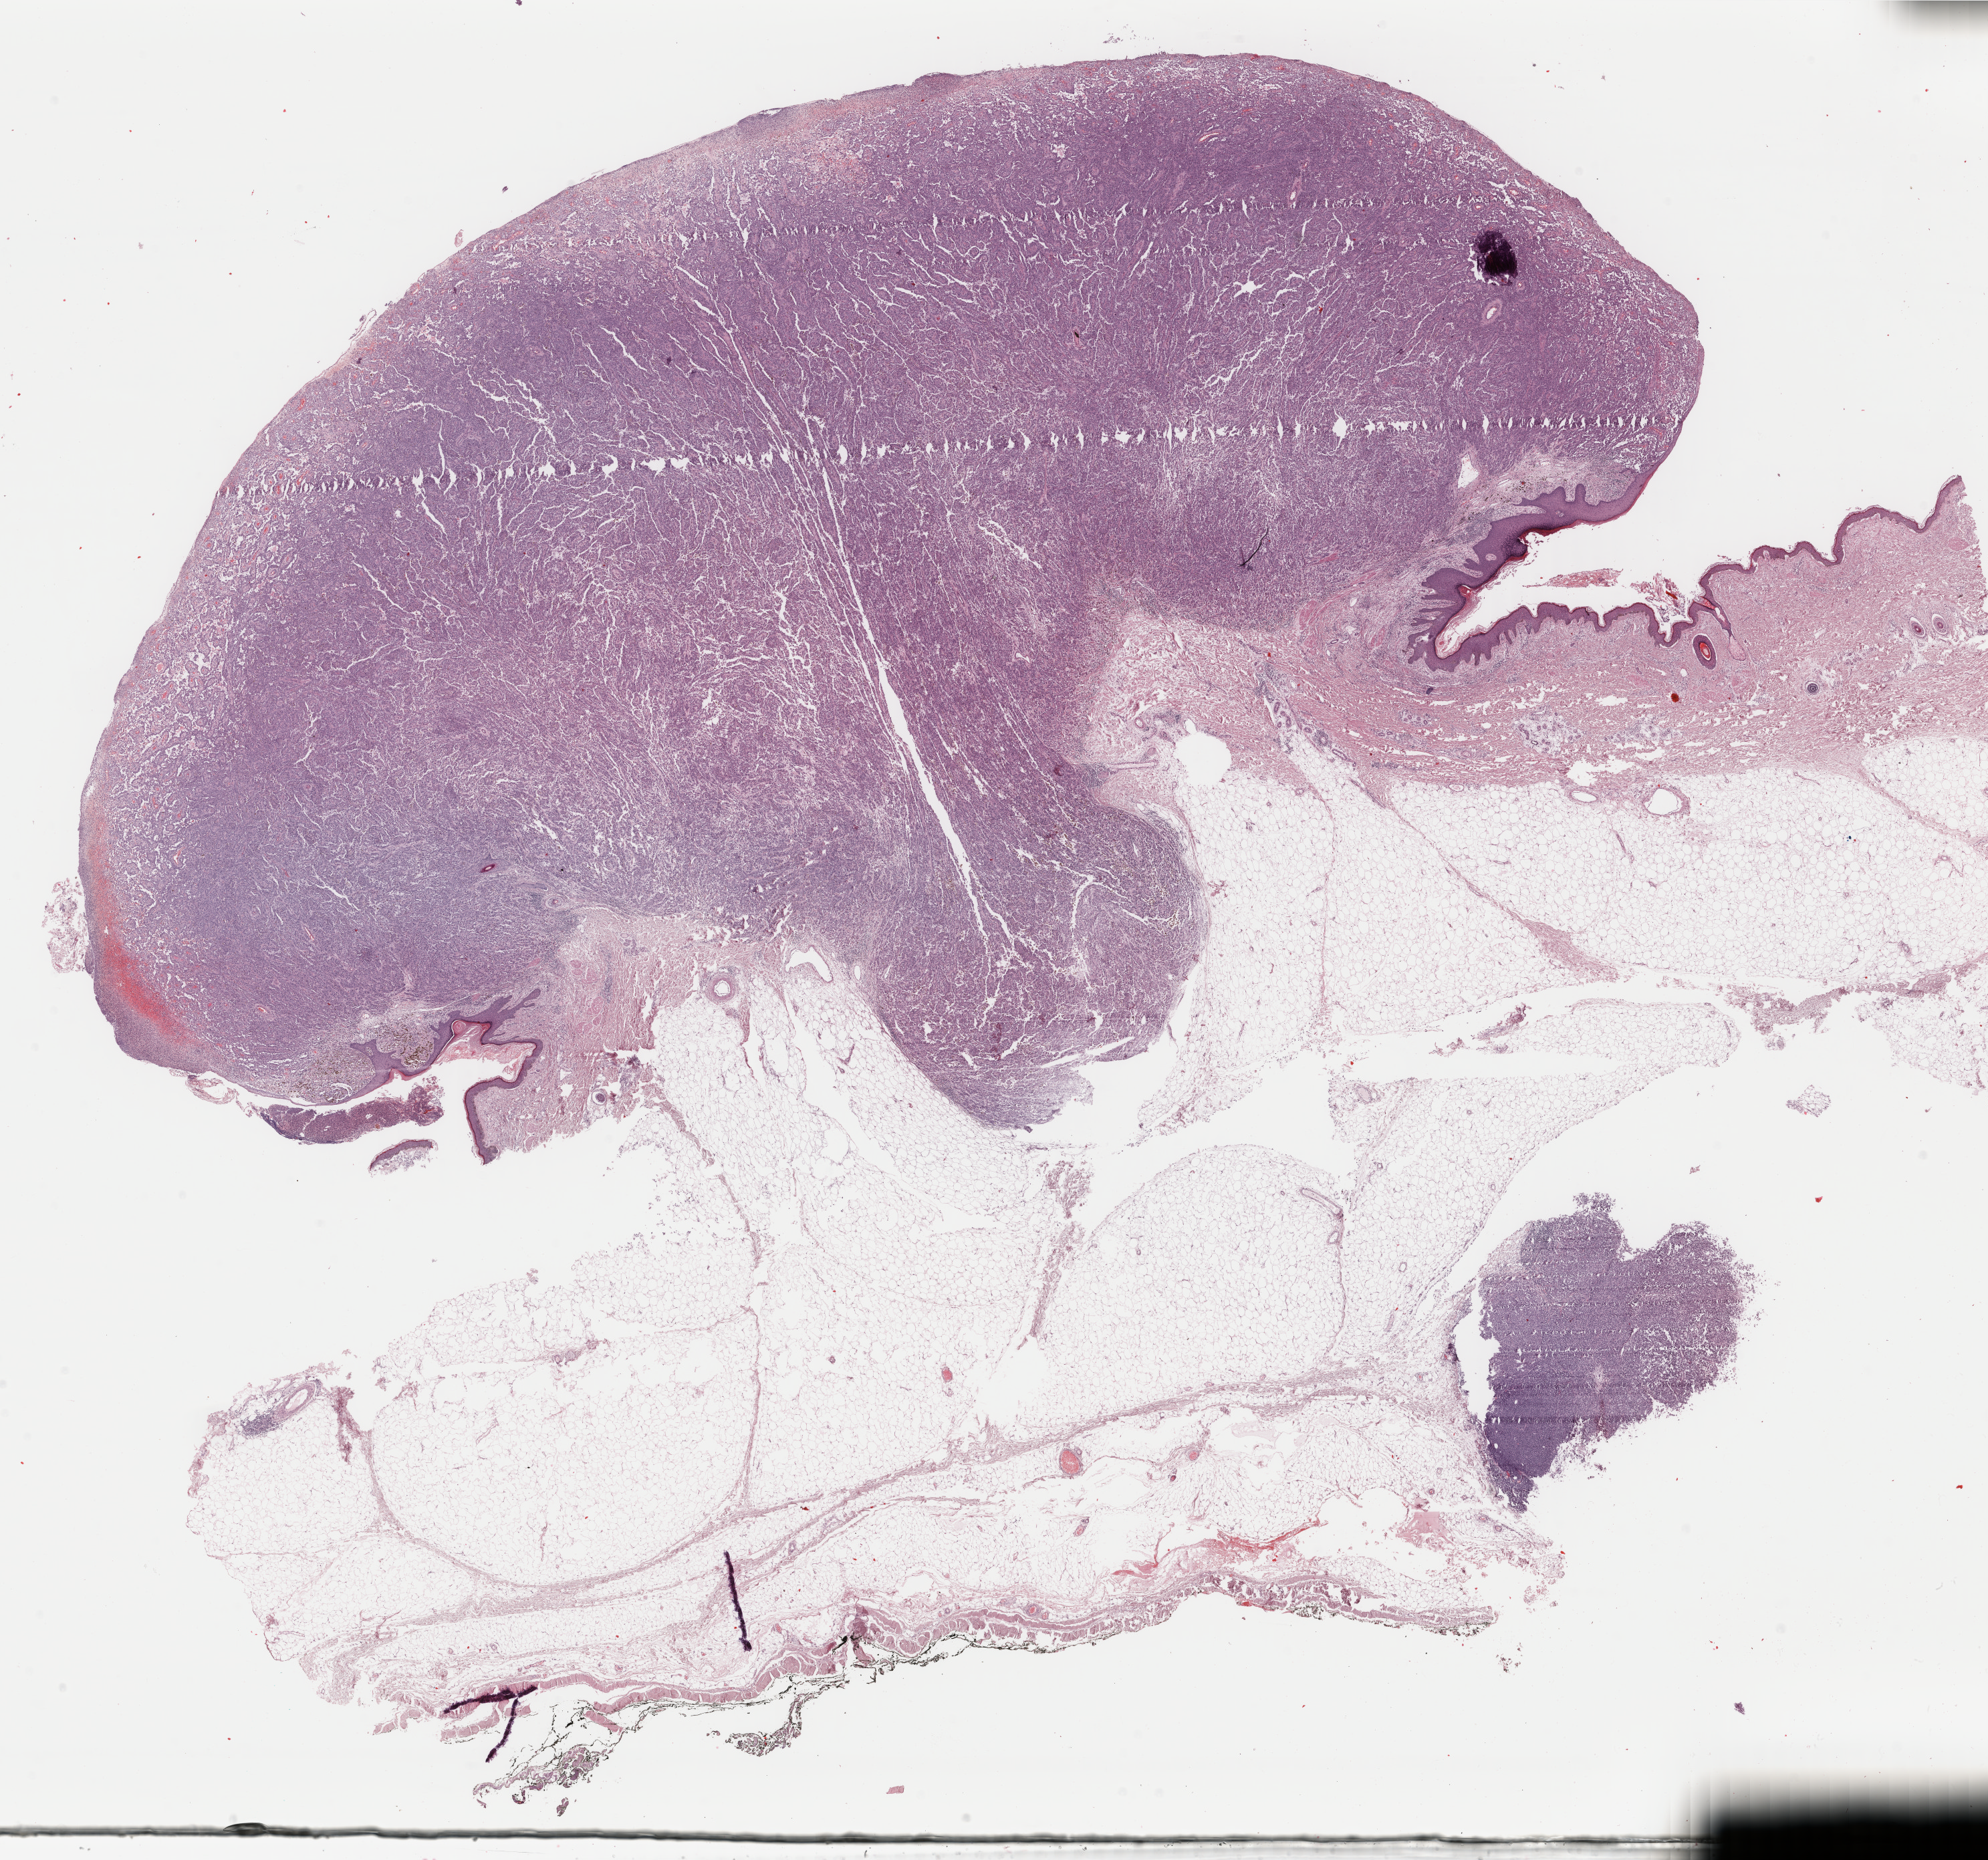
Whole-slide histology image, Hematoxylin and eosin (H&E) stained — a low-resolution overview of the entire scanned area, about 23.6 x 22.1 mm. Formalin-fixed paraffin-embedded (FFPE) diagnostic section. Primary tumour sample from the skin. Male patient; age at initial diagnosis 54 years.
Histologic diagnosis: Malignant melanoma, NOS.